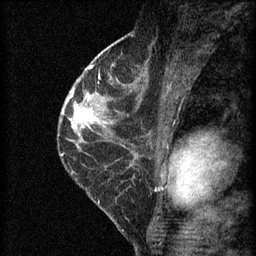
Breast MRI (dynamic contrast-enhanced), one sagittal slice; position 35 of 60 along the scan axis; 3 images stored at this slice position (order not interpretable as contrast timing); 1.5 T; TE 4.2 ms, TR 8.2 ms; 2 mm slice thickness; 256 × 256 image matrix, field of view 180 × 180 mm. Patient: female, 45 years.
Annotated regions visible in this slice (semi-automatically segmented with operator editing):
- analysis volume of interest (the breast-tissue region the enhancement analysis was run in; not a lesion): box from (x=62, y=98) to (x=104, y=139) px
- tumour enhancement mask (voxels above the 70 % enhancement threshold inside the analysis volume of interest): (x=63, y=98)–(x=98, y=127)